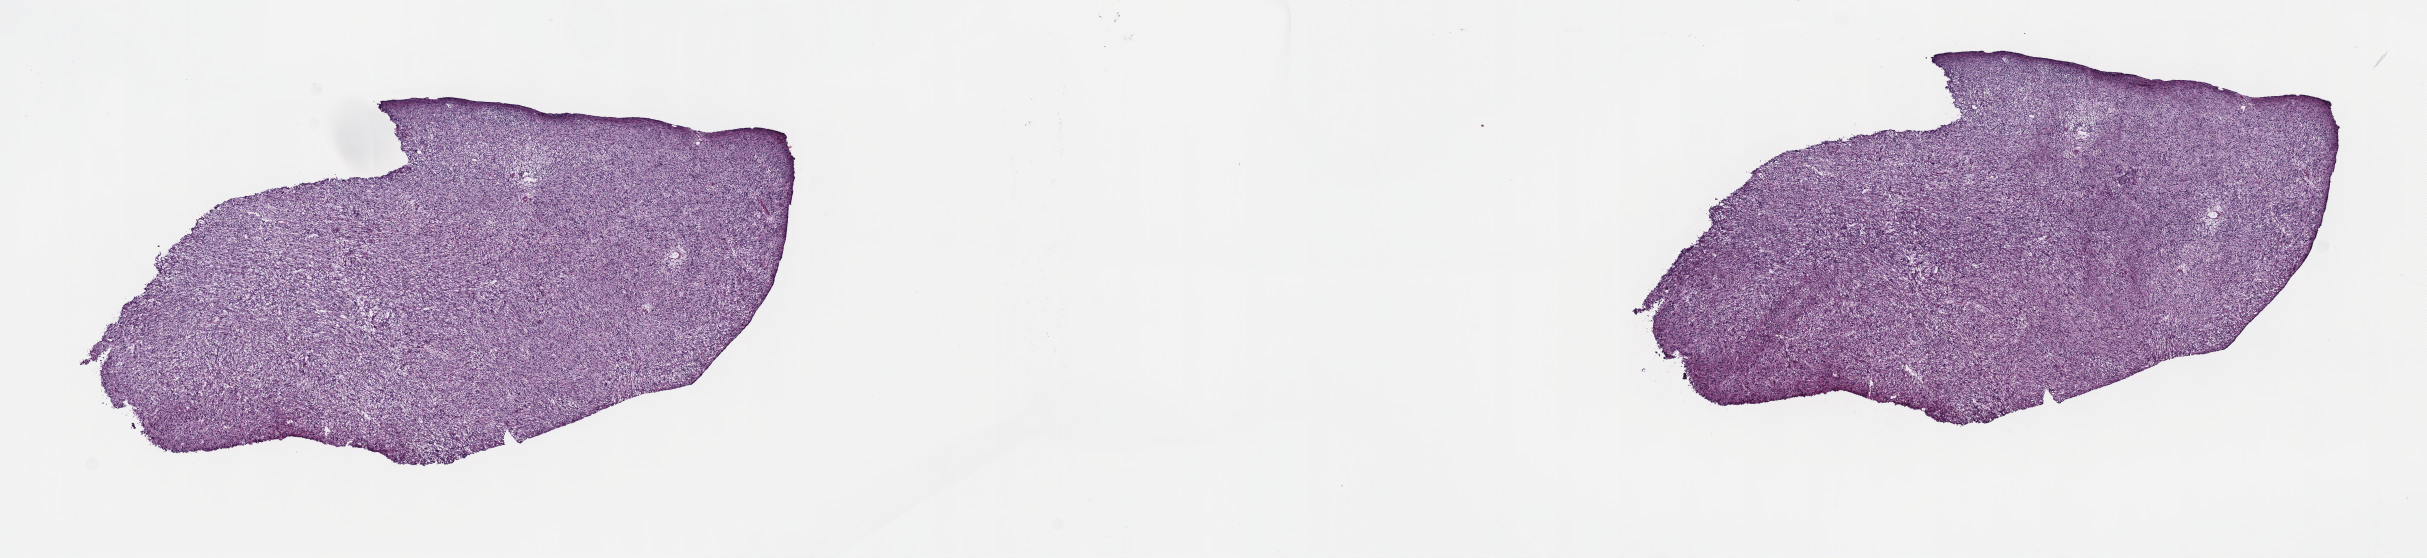
H&E-stained whole-slide image, low-resolution overview of the scanned area, about 19.6 x 4.5 mm (from a 40x scan). Frozen section from the top of the tissue portion. Primary tumour sample from the retroperitoneum and peritoneum. Male, age 75 years at initial diagnosis. Slide review estimates, as recorded: tumour cells 100%, tumour nuclei 80%, normal cells 0%, stromal cells 0%, necrosis 0%. Infiltration values recorded for this section: lymphocyte infiltration 1%, monocyte infiltration 0%, neutrophil infiltration 0%.
Pathologic diagnosis: Dedifferentiated liposarcoma.